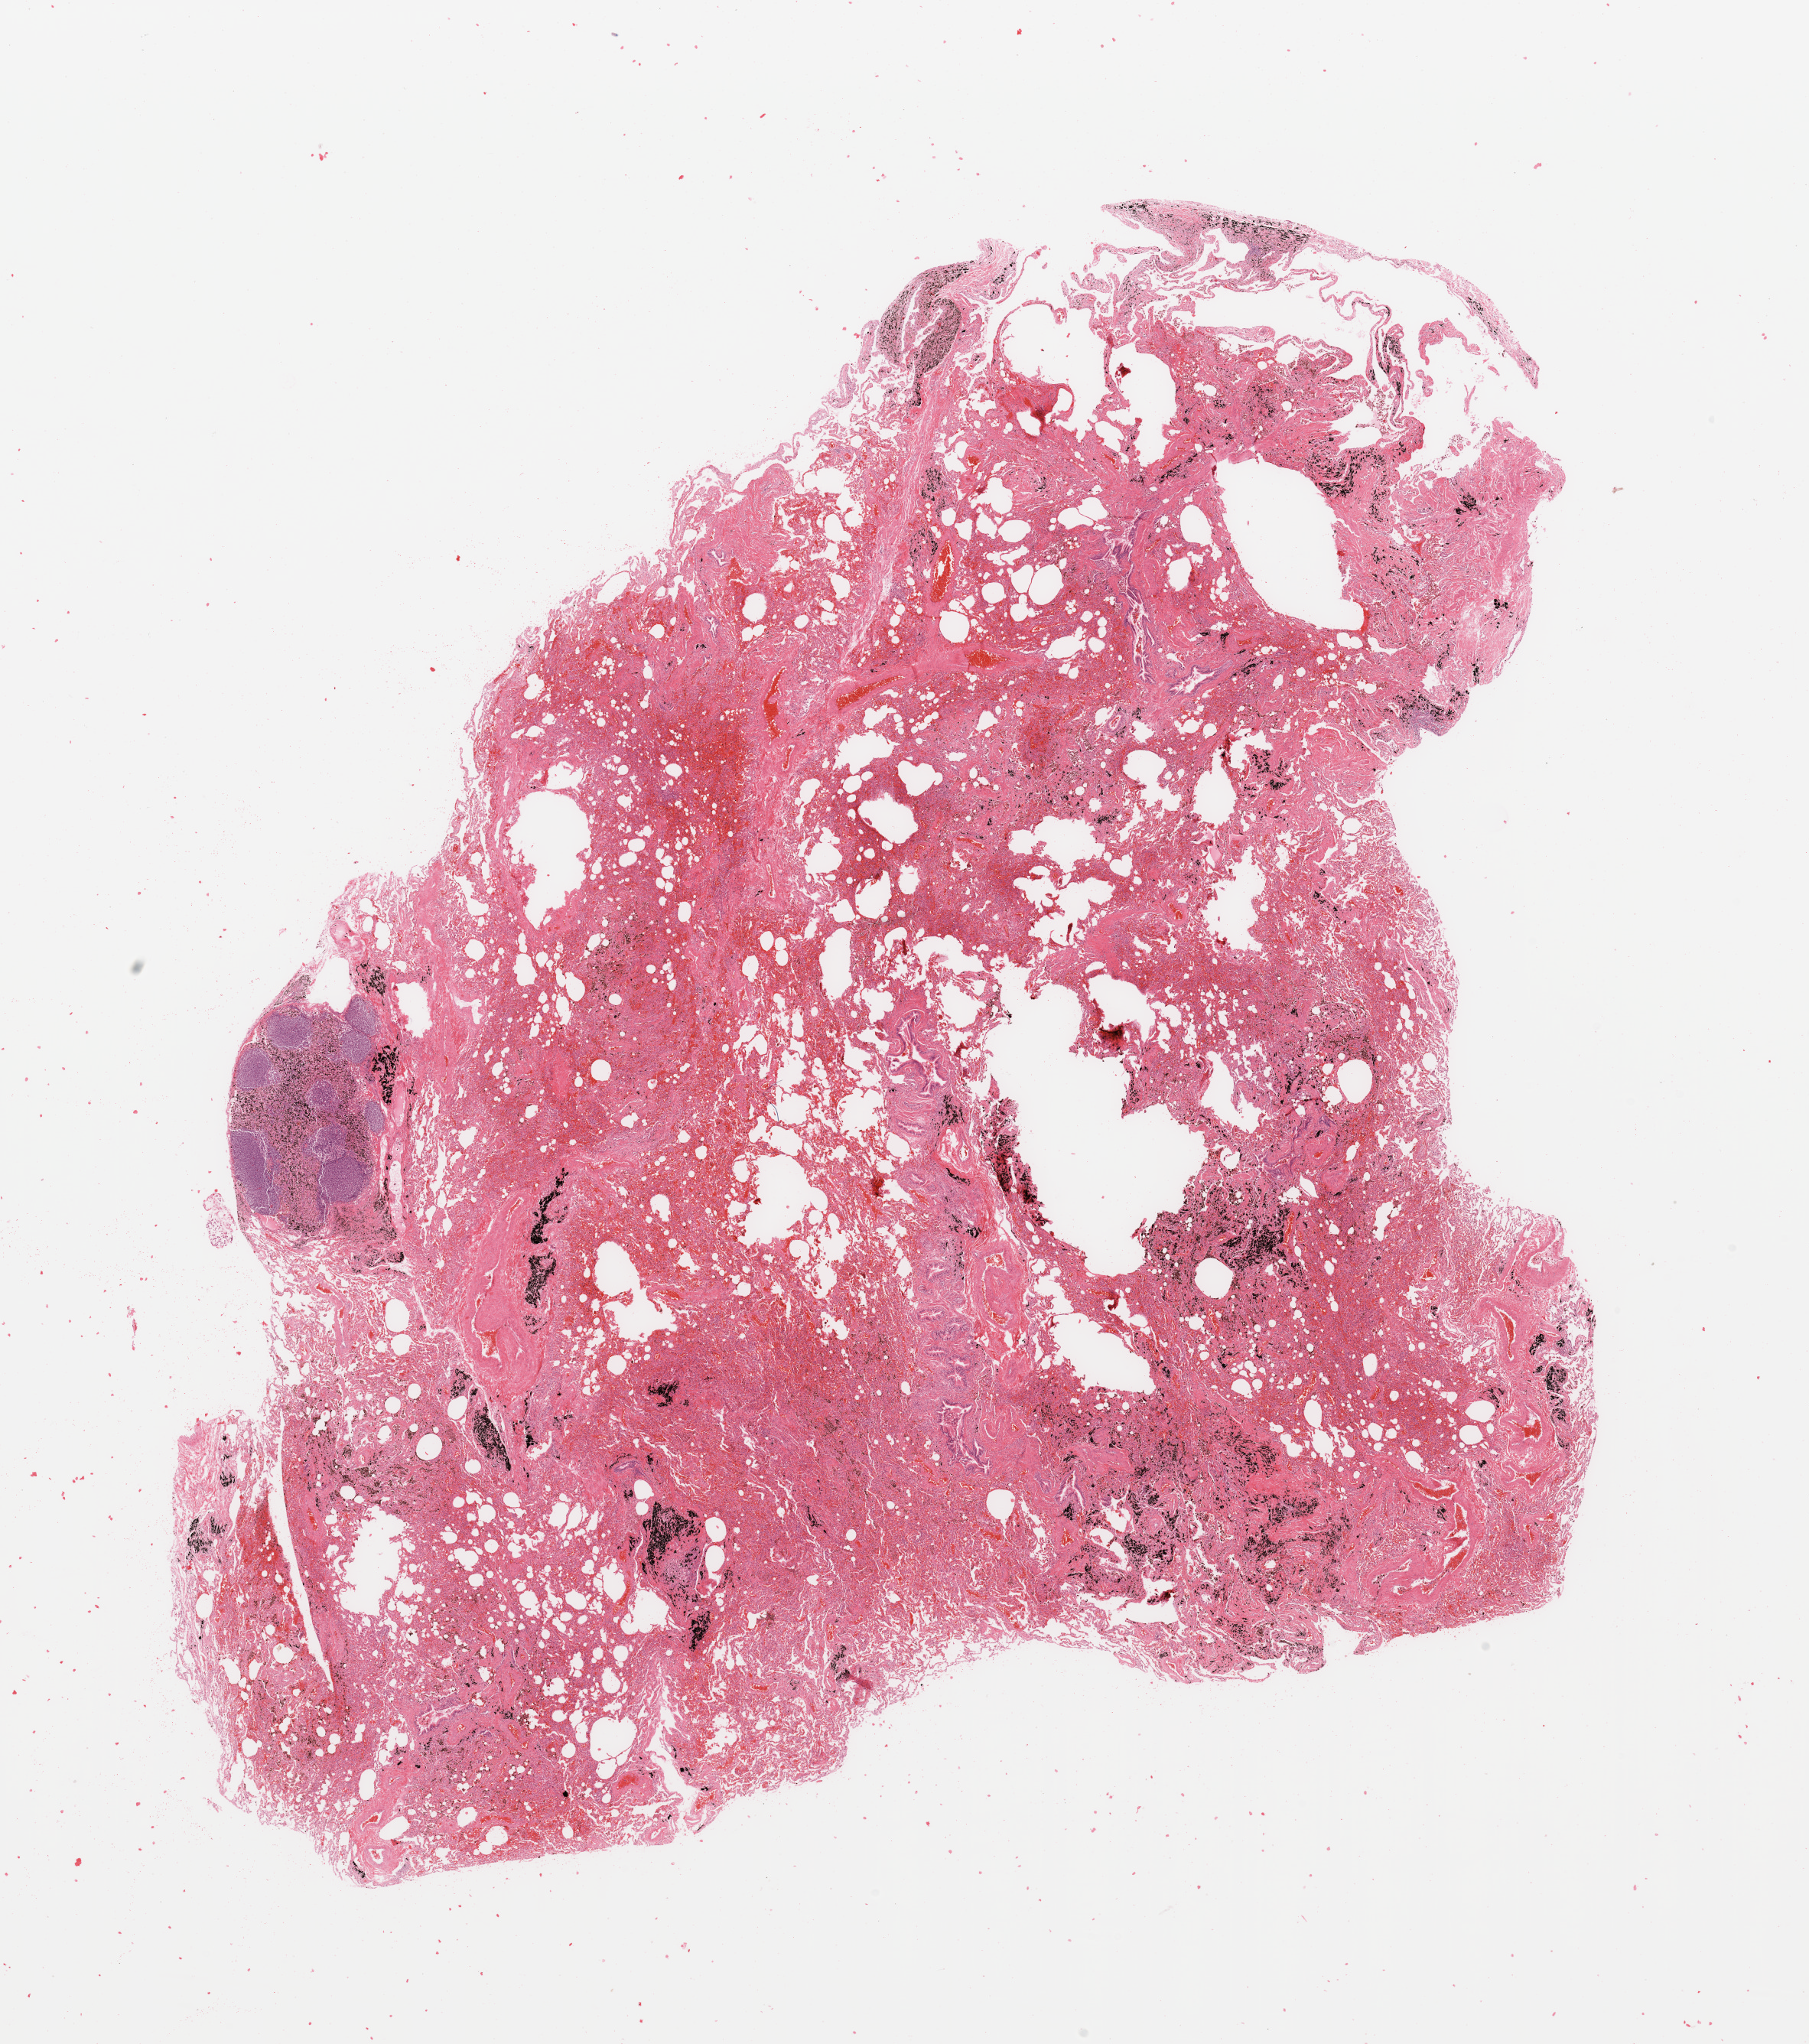
Whole-slide histology image, Hematoxylin and eosin (H&E) stained, low-resolution overview of the scanned area, about 18.7 x 21.1 mm (slide scanned at 20x). Normal (non-tumour) tissue sample, lung. Male, 56 y/o.
This section: normal (non-tumour) tissue from the same patient. Patient diagnosis: Adenocarcinoma, NOS.